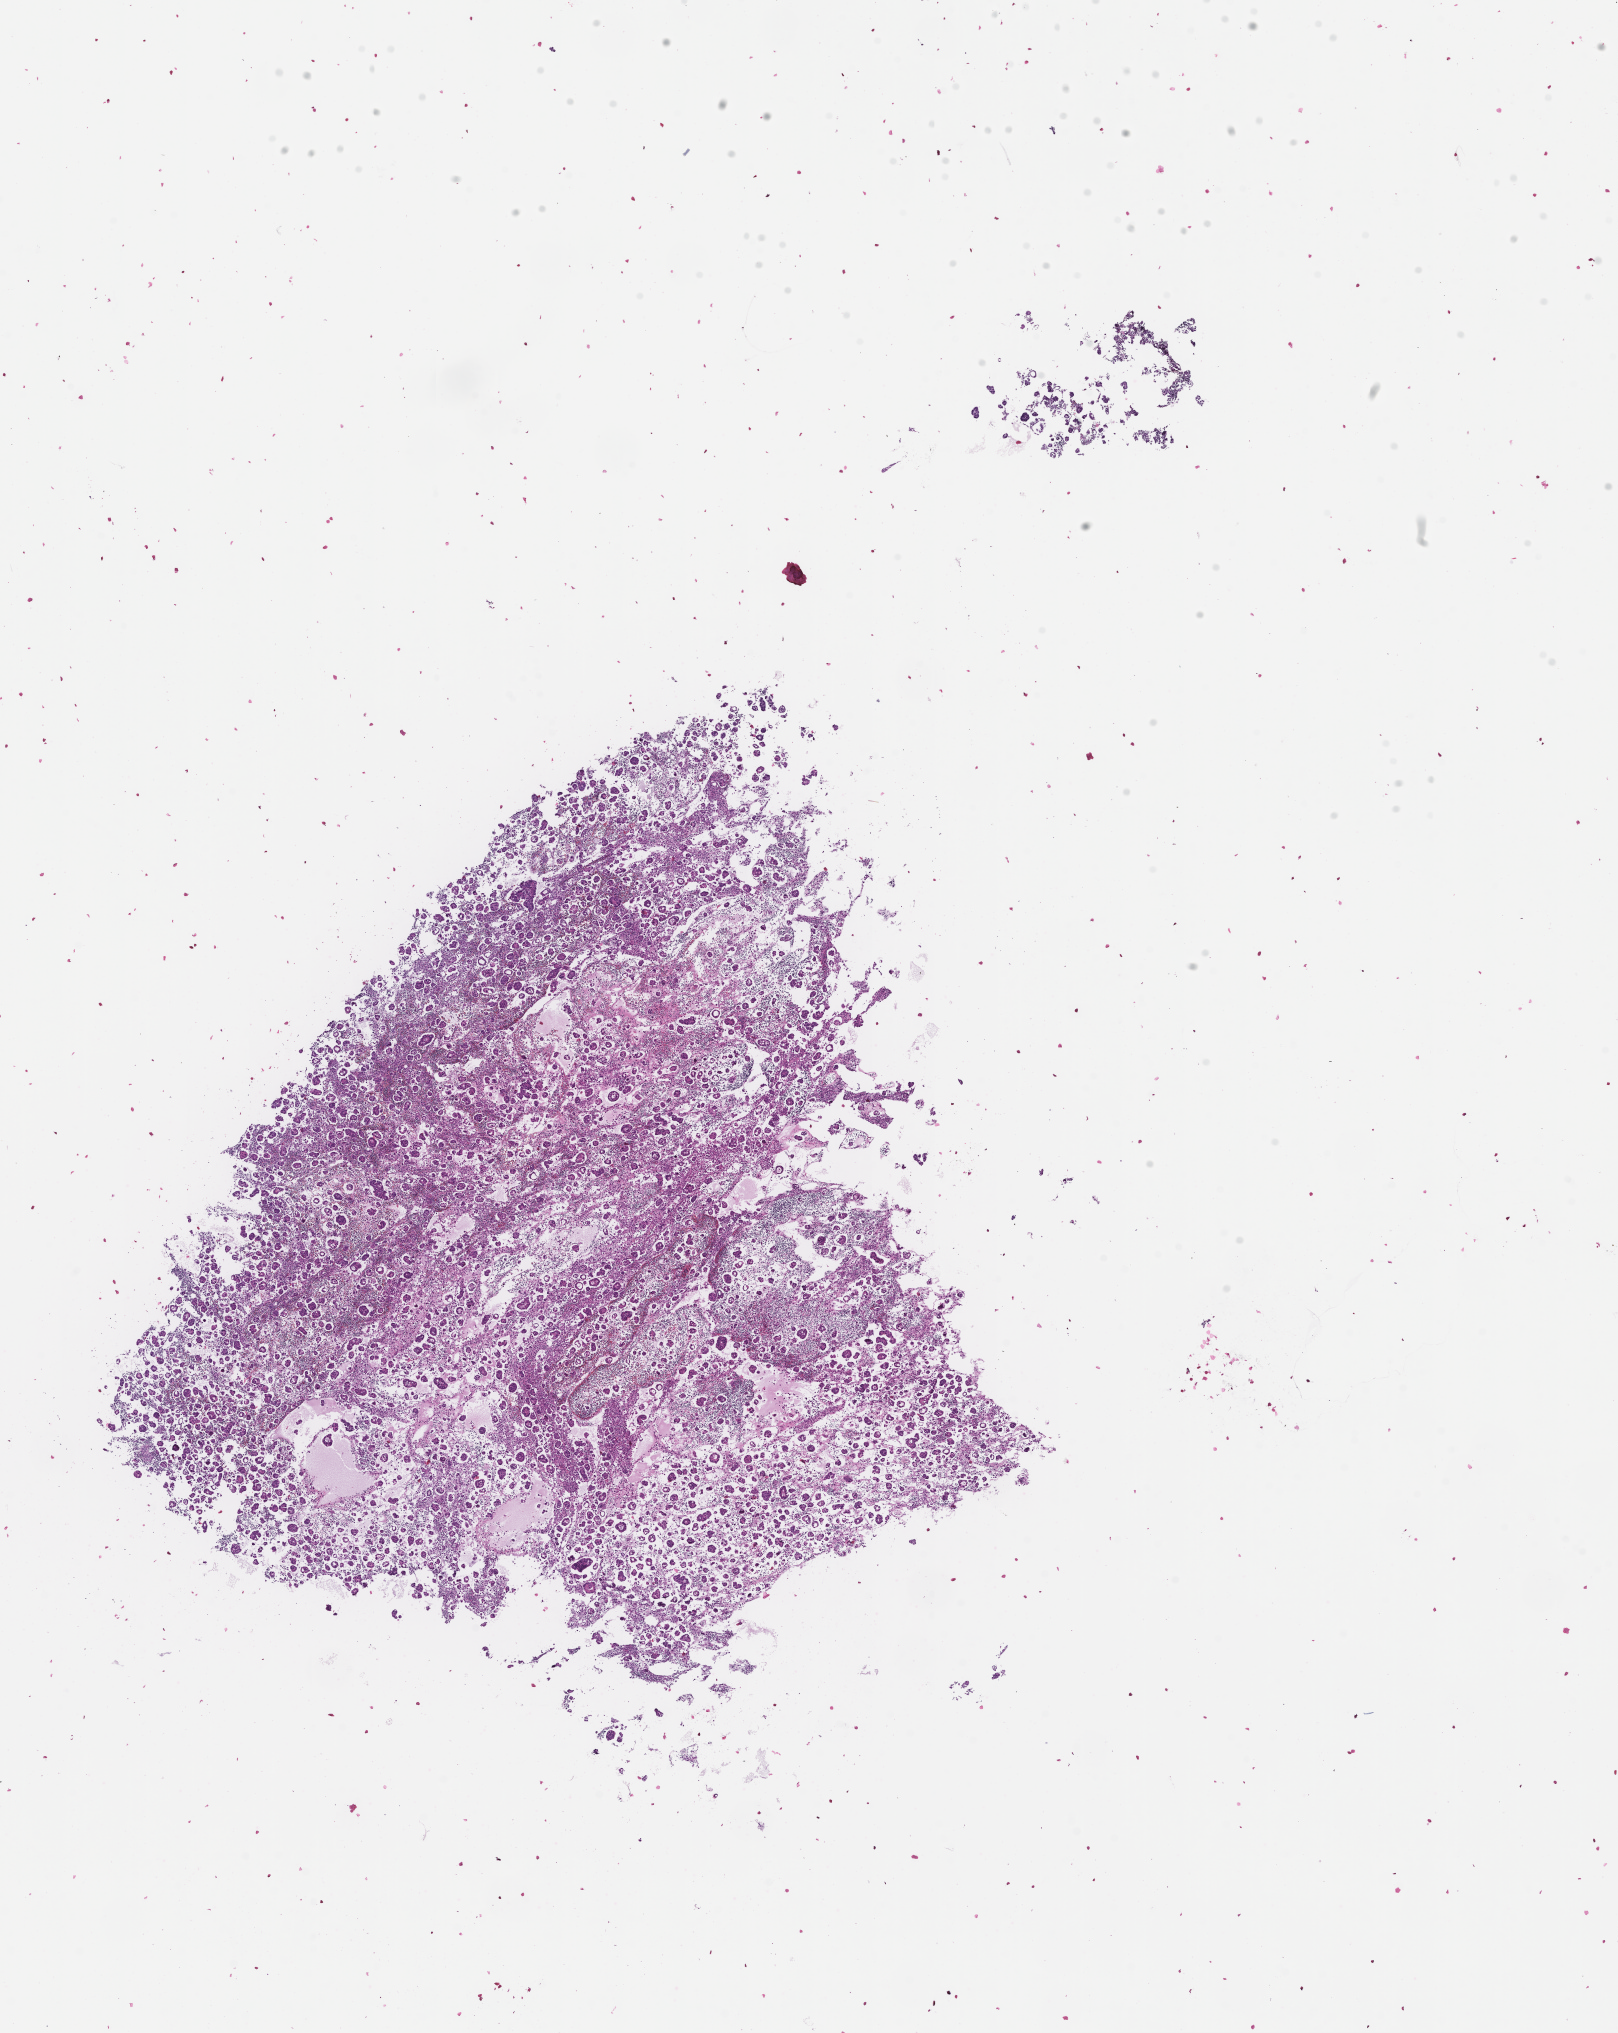
Whole-slide image, hematoxylin and eosin (H&E) stain, whole scanned area (about 13.1 x 16.4 mm) shown as a low-resolution overview, formalin-fixed, paraffin-embedded (FFPE) tissue, archival tissue. Patient sex: female.
- this section: metastasis (sampled organ not recorded)
- patient diagnosis (primary): Invasive Breast Carcinoma